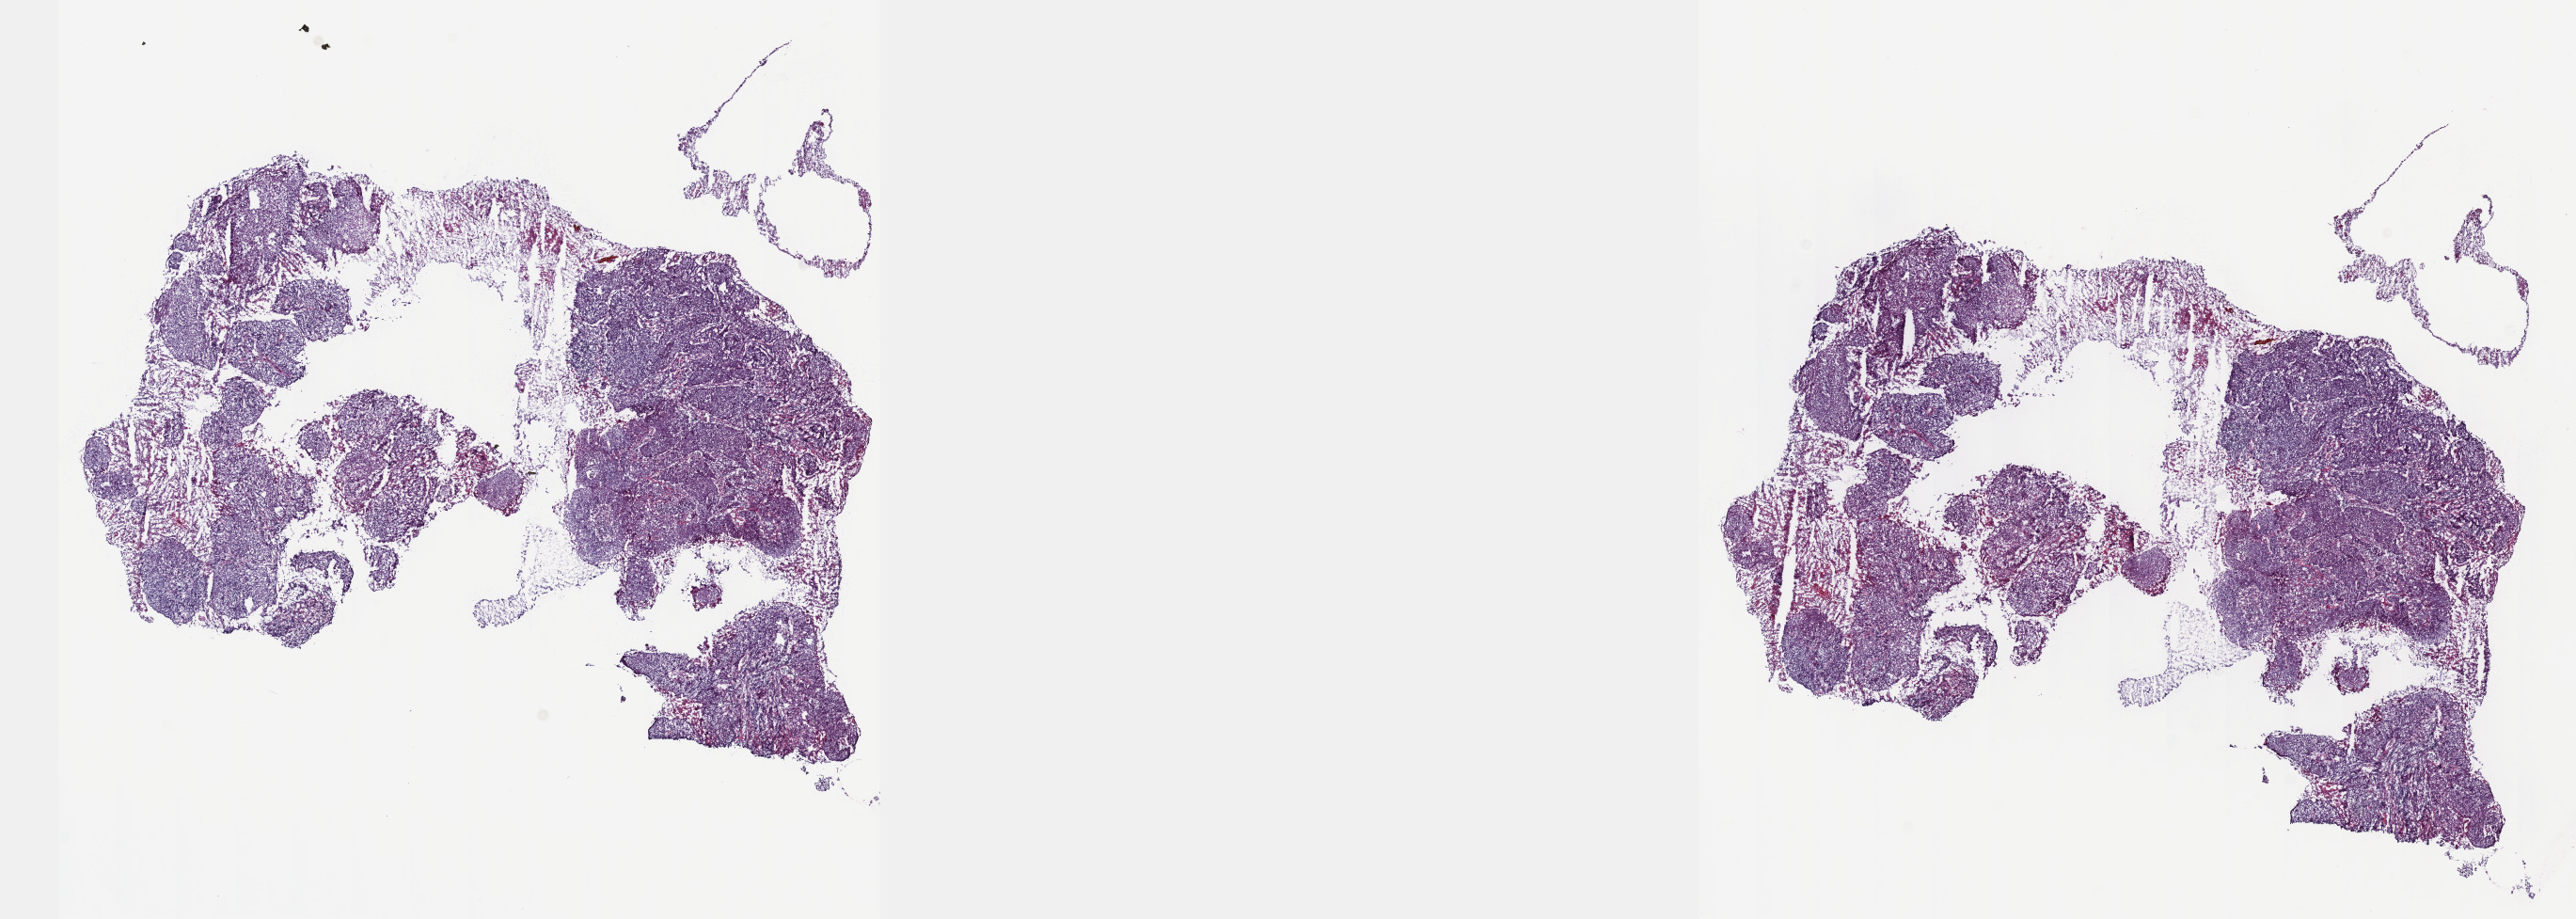
Hematoxylin and eosin (H&E) stained whole-slide image — low-resolution overview of the scanned area, about 22.1 x 7.9 mm (from a 40x scan). Frozen section from the top of the tissue portion. Cervix, primary tumour sample. Female, age 54 years at initial diagnosis. Histologic grade: G2 (moderately differentiated). Pathologist review of this section (percent, as recorded): tumour cells 80%, tumour nuclei 90%, normal cells 0%, stromal cells 20%, necrosis 0%. Inflammatory infiltration, as recorded: lymphocyte infiltration 0%, monocyte infiltration 0%, neutrophil infiltration 0%.
- FIGO stage: IIIB
- pathologic diagnosis: Squamous cell carcinoma, large cell, nonkeratinizing, NOS (cervix uteri)